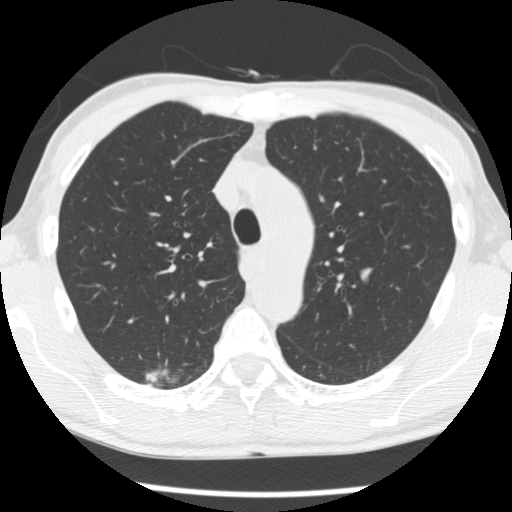
Low-dose screening chest CT, axial slice. Baseline annual screen. Lung window (W 1500 / L -600 HU). 2.5 mm slice thickness. Standard (soft-tissue) reconstruction kernel (STANDARD). 120 kVp. Slice 76 of 277 in the series. Male, age 66 years at enrolment. Former smoker at enrolment.
Expert-annotated lung lesion, bounding box <135,356,187,395> (left, top, right, bottom; pixels). The screening reader recorded 4 non-calcified nodules or masses ≥4 mm on this exam (right upper lobe, right upper lobe, right upper lobe, left lower lobe); which of them this box marks is not recorded. Later outcome: lung cancer diagnosed 503 days after this screen — adenocarcinoma, NOS, right upper lobe, undifferentiated (G4), stage IA (AJCC 6th edition), 20 mm at pathology.